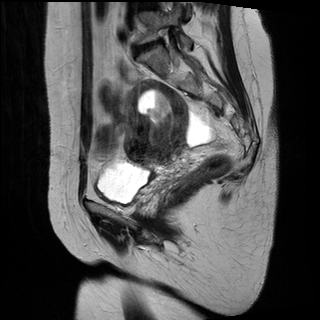
Pelvic MRI for cervical cancer, one sagittal slice; position 20 of 34 along the scan axis; T2-weighted; 1.5 T; TE 89 ms, TR 3320 ms; 4 mm slice thickness; 320 × 320 image matrix, field of view 260 × 260 mm. Female patient, age 49 years.
Structures marked on this image (expert manual segmentation):
- uterus and cervix: bounding box <123,78,189,164> (left, top, right, bottom; pixels)